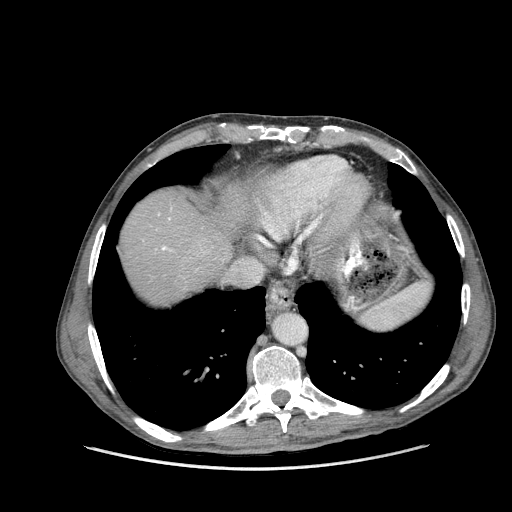
Contrast-enhanced abdominal CT (liver protocol), one axial slice. Slice 135 of 162 in the series (ordered by position). Reconstruction kernel STANDARD. 100 kVp. Soft-tissue window (W 400 / L 40 HU). 2.5 mm slice thickness. 512 × 512 image matrix. From the clinical record (not read from this slice): diagnosis: hepatocellular carcinoma (patient treated with transarterial chemoembolisation; whether this scan precedes or follows treatment is not stated here); TNM stage (as recorded): Stage-IIIA; Child-Pugh class: A; tumour size: 9.9 cm.
Structures marked on this image (semi-automatically segmented with operator editing):
- abdominal aorta: bounding box (x1, y1, x2, y2) in pixels: (275, 314, 306, 345)
- liver parenchyma outside the tumour (the mass and vessels are separate outlines, so this box may not span the whole liver): (120, 190, 232, 304)
- liver vessels: (162, 218, 171, 250)